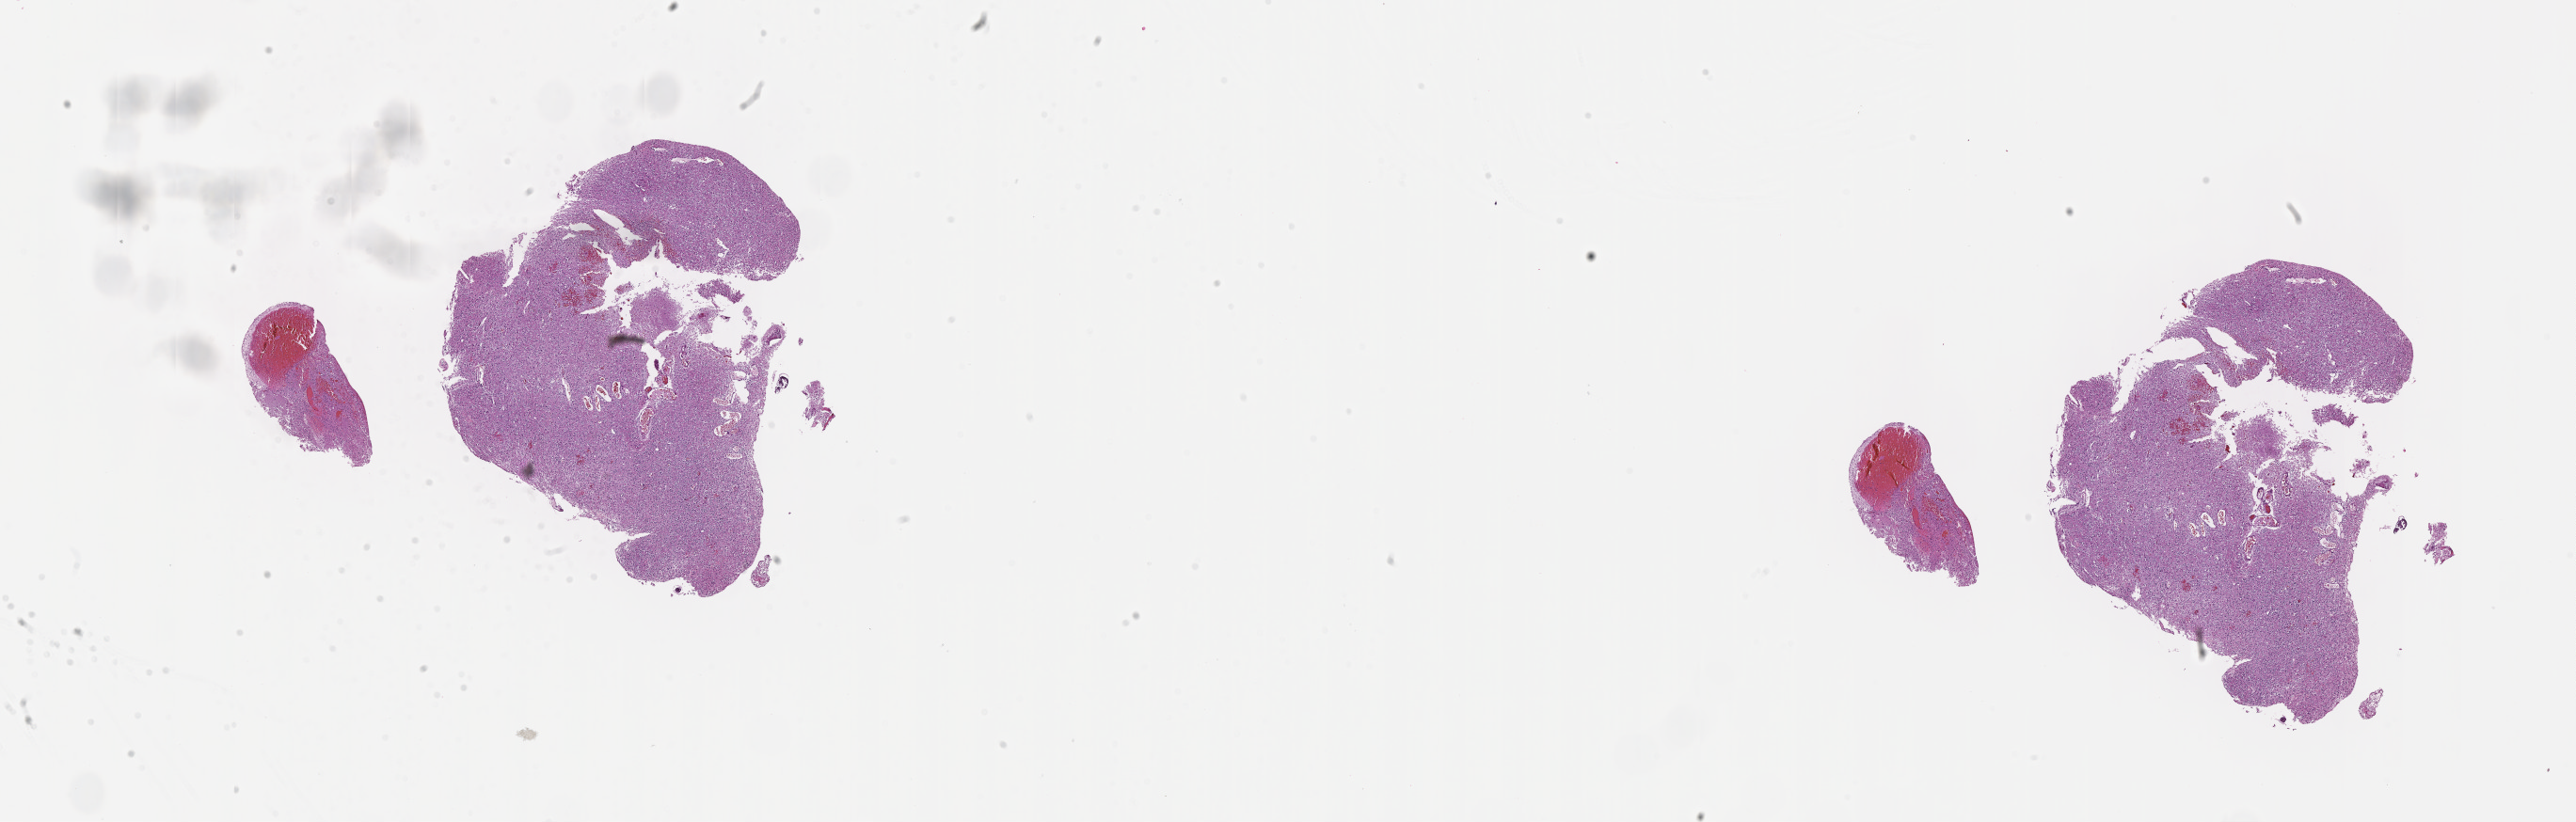
Digitized H&E-stained tissue section (whole slide), a low-resolution overview of the entire scanned area, about 22.1 x 7.1 mm, formalin-fixed paraffin-embedded (FFPE) diagnostic section, brain, primary tumour sample. Patient: female, age at initial diagnosis 37 years. Histologic grade: G2 (moderately differentiated).
Diagnosis: Oligodendroglioma, NOS (cerebrum). Laterality: right.